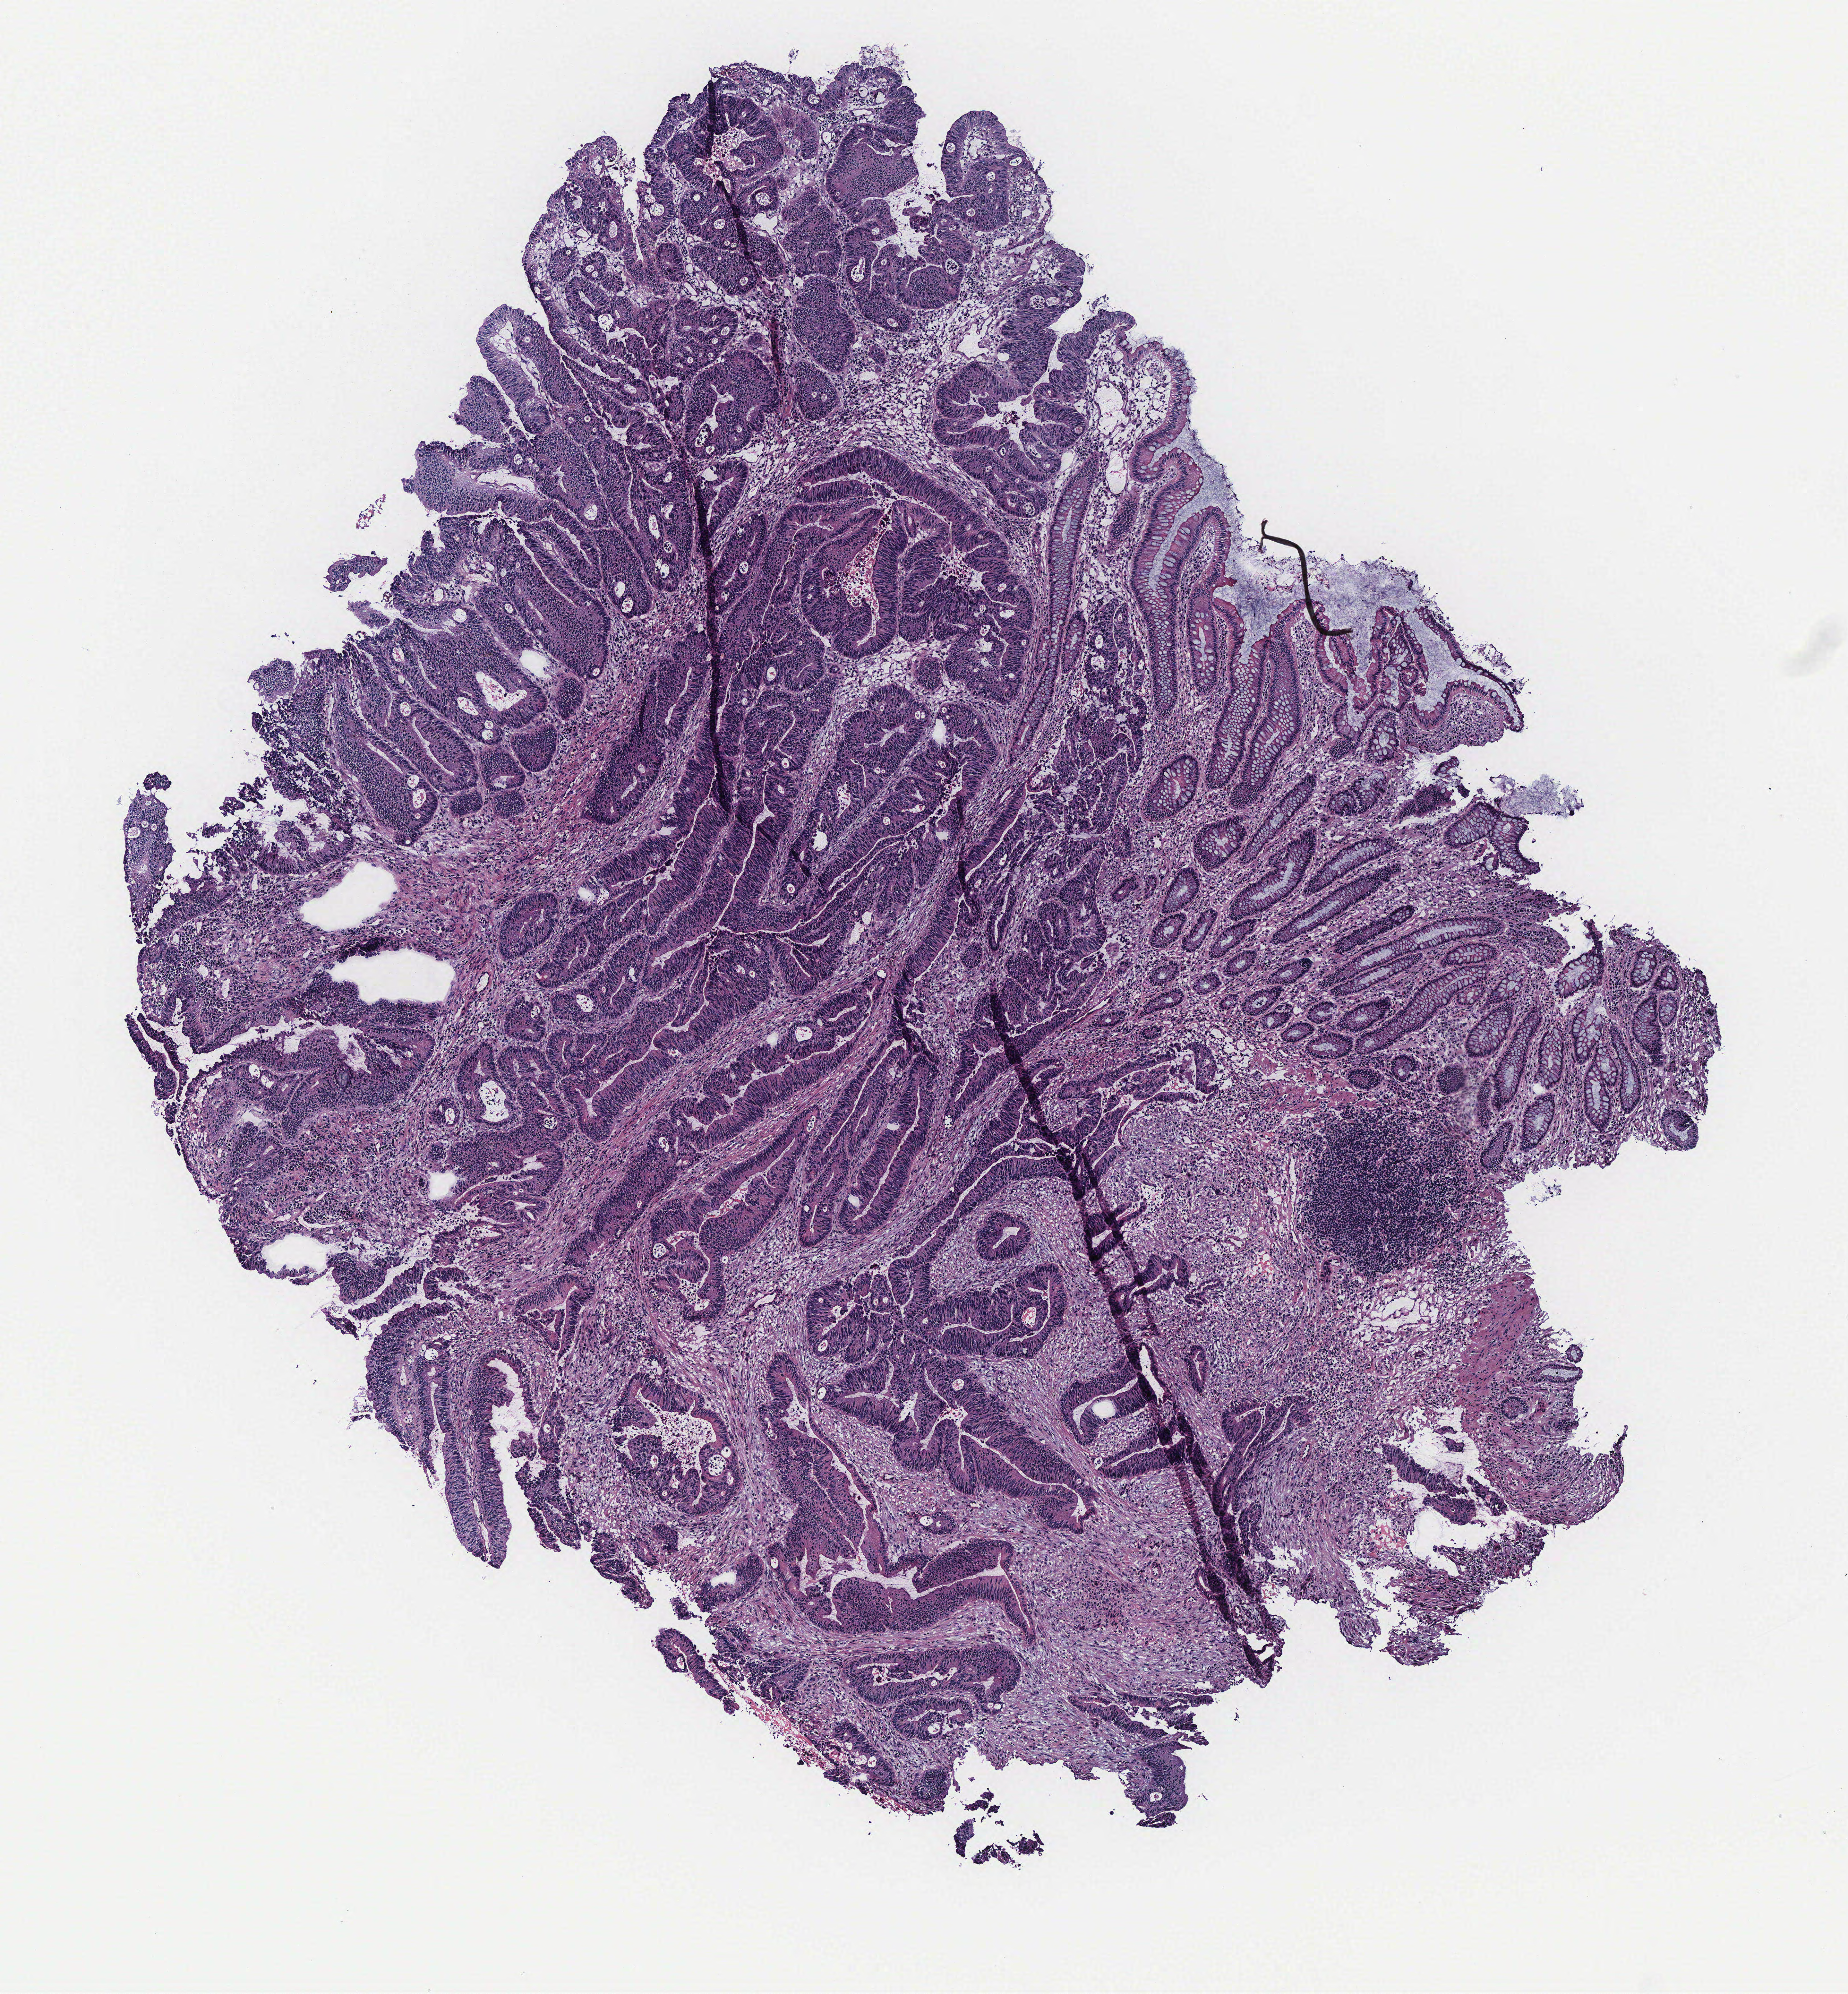
Digitized H&E-stained tissue section (whole slide), a low-resolution overview of the entire scanned area, about 5.8 x 6.2 mm, tumour tissue sample, colon. 86-year-old male patient.
- primary tumour site (as recorded): colon
- histologic diagnosis: Adenocarcinoma, NOS
- AJCC pathologic stage: I